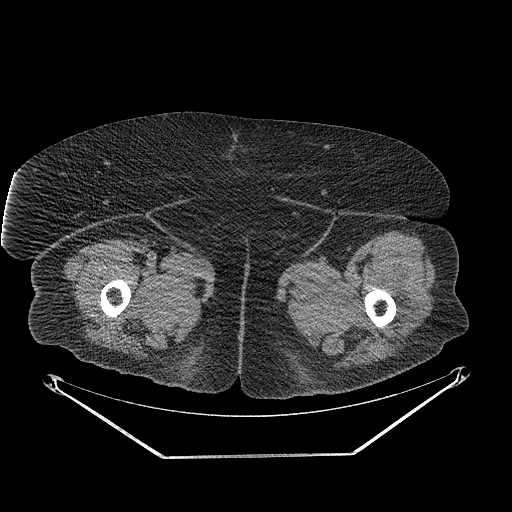
CT of an extremity soft-tissue mass (from a PET/CT study), one axial slice; slice 260 of 267 in the series (ordered by position); reconstruction kernel STANDARD; soft-tissue window (W 400 / L 40 HU); 3.75 mm slice thickness; 512 × 512 image matrix, field of view 500 × 500 mm. Female patient. Case-level facts recorded for this patient, not image findings: histological type: undifferentiated – high grade; grade: high; site of the primary tumour: left thigh.
Structures marked on this image (expert contour drawn on MRI and transferred to this co-registered scan by the dataset authors):
- gross tumour volume including surrounding oedema: box from (x=397, y=297) to (x=416, y=316) px